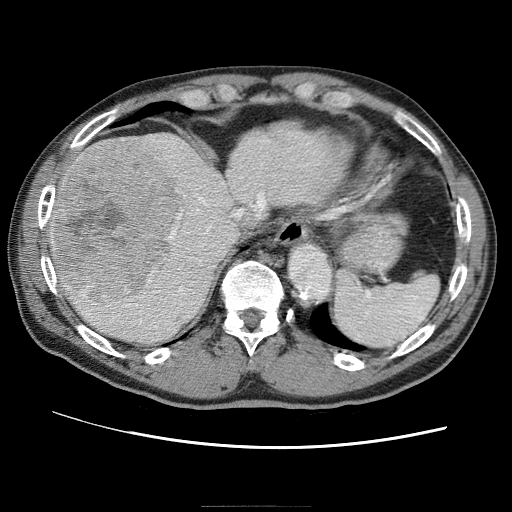
Contrast-enhanced abdominal CT (liver protocol), one axial slice. Slice 52 of 75 in the series (ordered by position). 120 kVp. One of 2 acquisitions stored at this slice position. Soft-tissue window (W 400 / L 40 HU). 2.5 mm slice thickness. 512 × 512 image matrix, field of view 360 × 360 mm. From the clinical record (not read from this slice): diagnosis: hepatocellular carcinoma (patient treated with transarterial chemoembolisation; whether this scan precedes or follows treatment is not stated here); TNM stage (as recorded): Stage-II; Child-Pugh class: A; tumour size: 2 cm.
Structures marked on this image (semi-automatic segmentation, software-assisted and operator-edited):
- abdominal aorta: box from (x=288, y=243) to (x=330, y=299) px
- liver parenchyma outside the tumour (the mass and vessels are separate outlines, so this box may not span the whole liver): (x=46, y=118)–(x=358, y=346)
- mass: (x=53, y=141)–(x=186, y=304)
- liver vessels: (x=53, y=160)–(x=316, y=318)